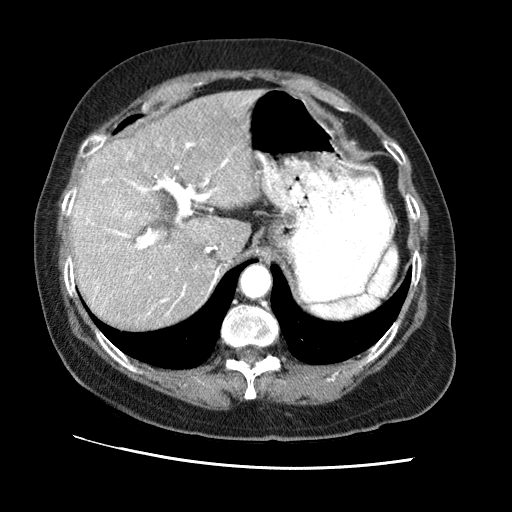
Contrast-enhanced abdominal CT (liver protocol), one axial slice. 120 kVp. Soft-tissue window (W 400 / L 40 HU). 512 × 512 image matrix. Case-level facts recorded for this patient, not image findings: diagnosis: hepatocellular carcinoma (patient treated with transarterial chemoembolisation; whether this scan precedes or follows treatment is not stated here); TNM stage (as recorded): Stage-II; Child-Pugh class: A; tumour differentiation: no biopsy; tumour nodularity: multinodular.
Outlined on this slice (semi-automatically segmented with operator editing):
- liver parenchyma outside the tumour (the mass and vessels are separate outlines, so this box may not span the whole liver): box from (x=70, y=90) to (x=262, y=328) px
- liver vessels: (x=75, y=142)–(x=229, y=315)